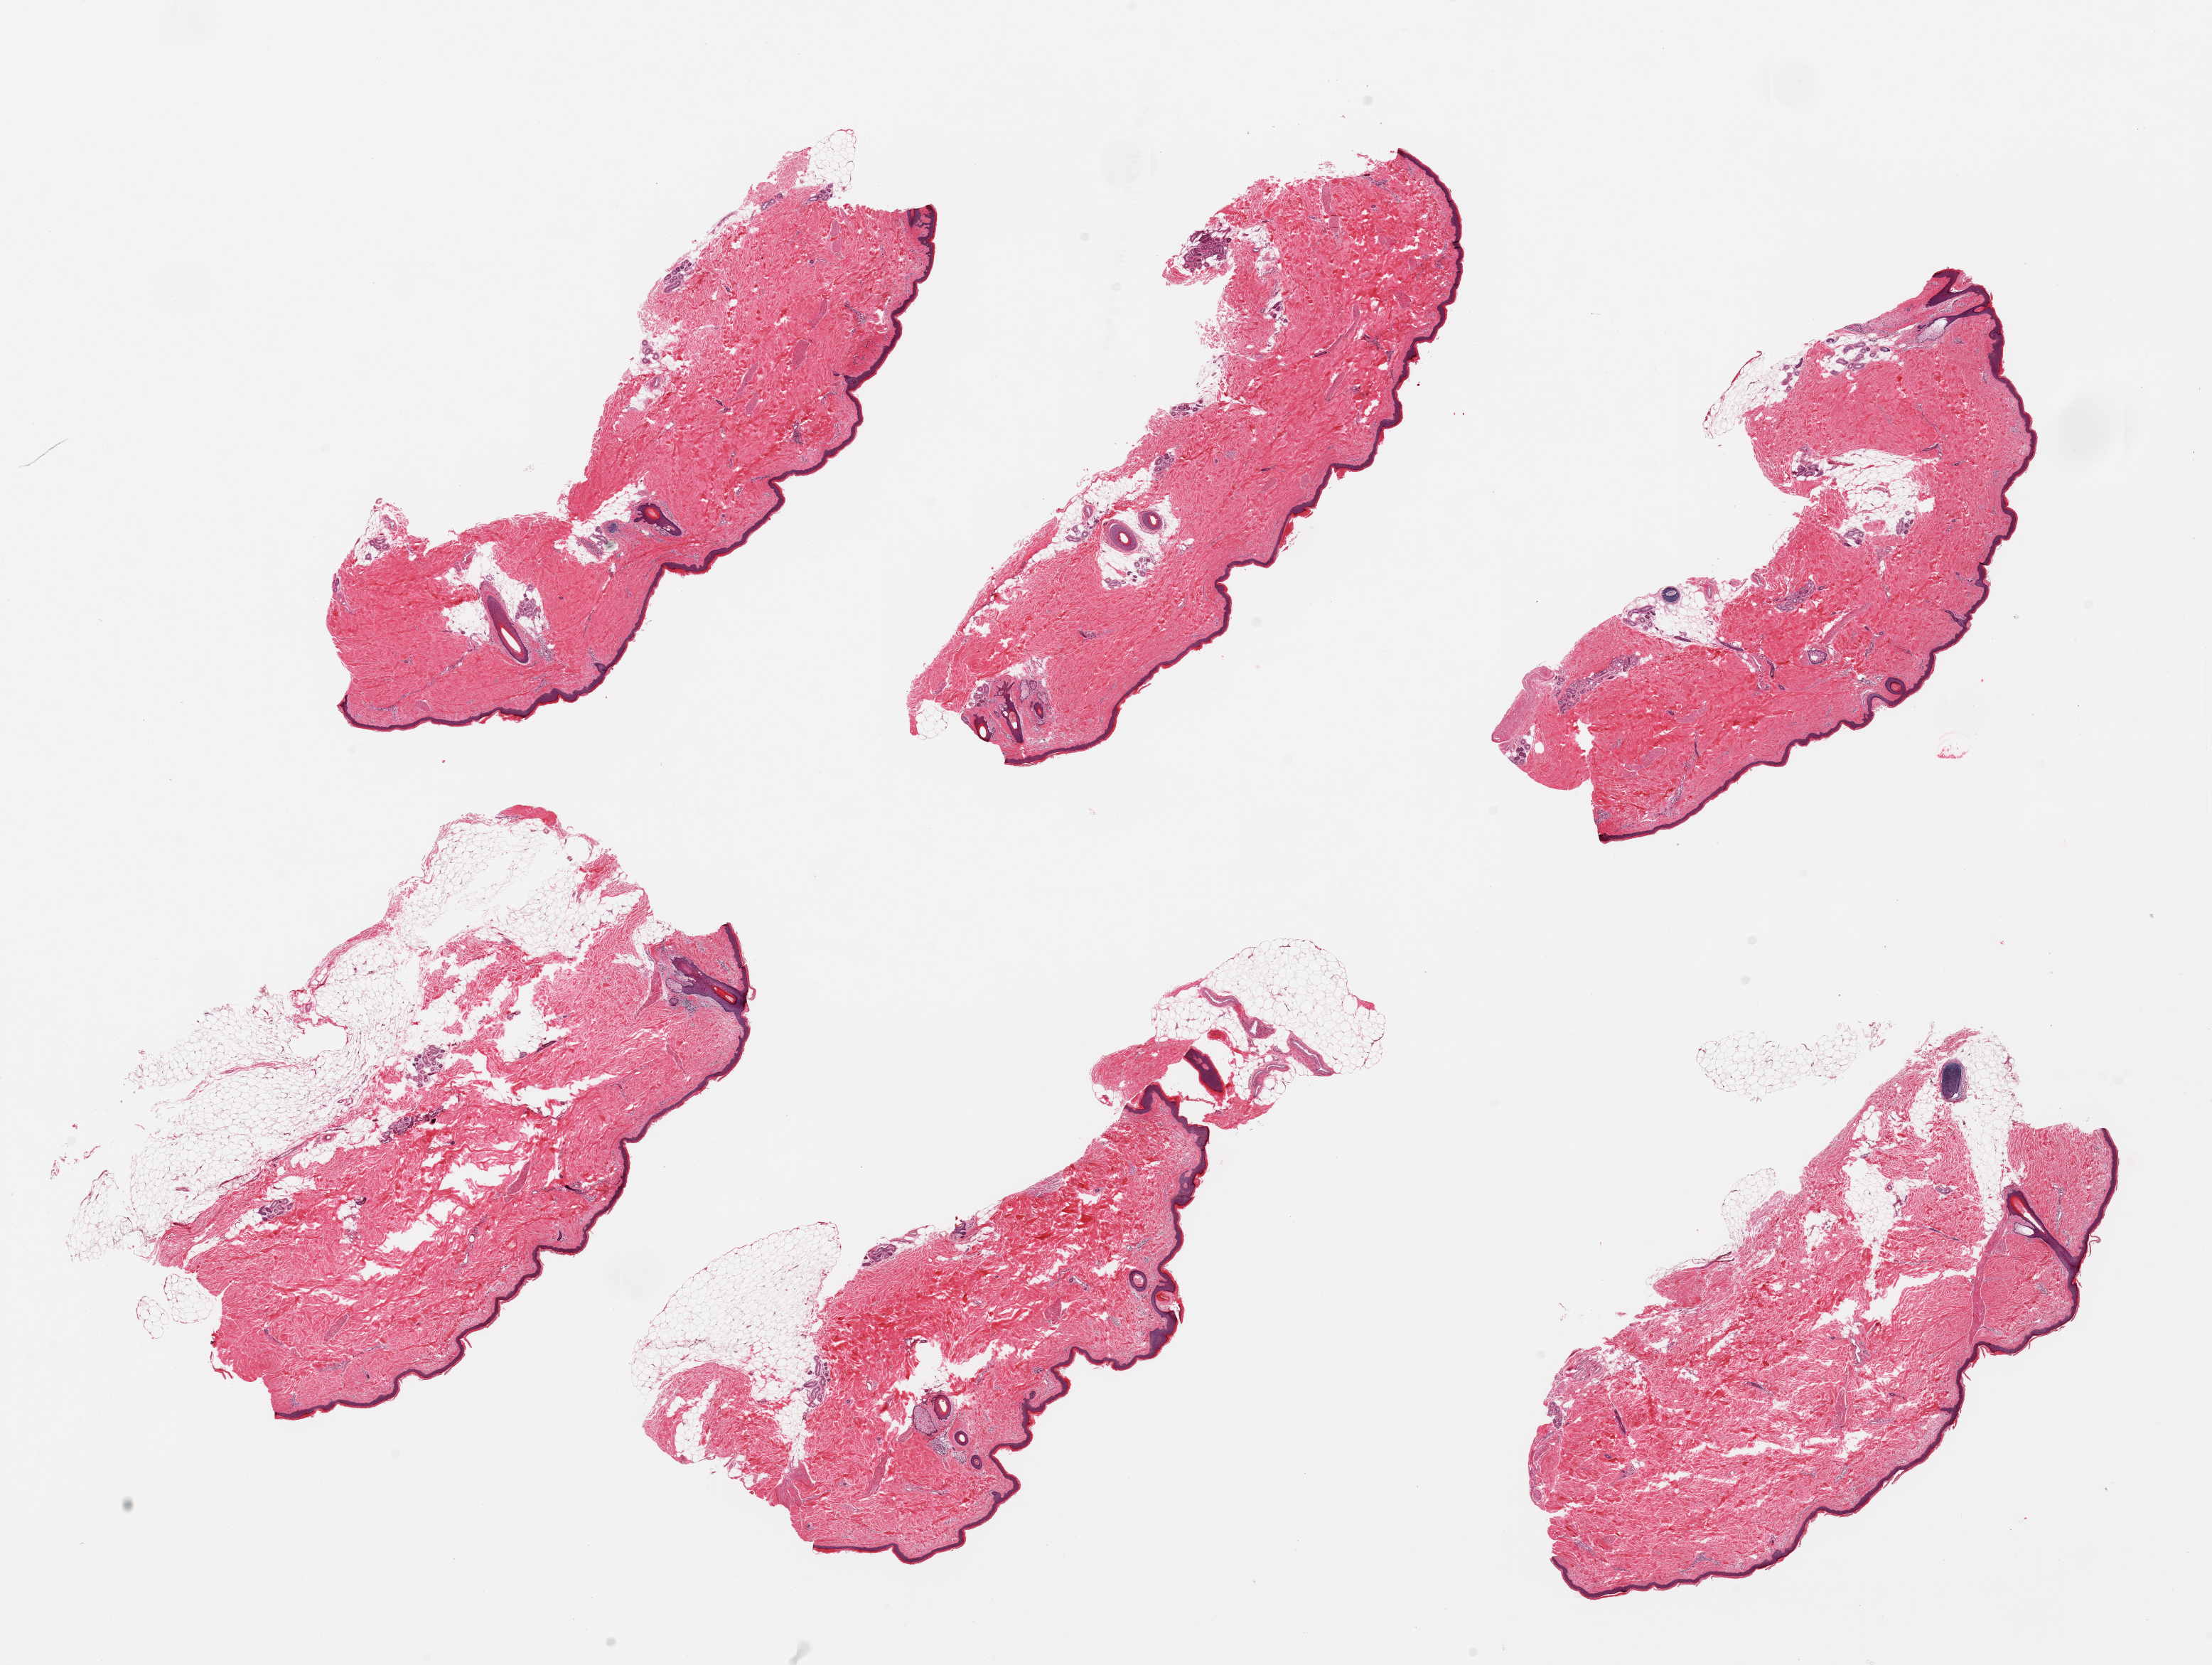
Whole-slide image, hematoxylin and eosin (H&E) stain — low-resolution overview of the scanned area, about 24.6 x 18.5 mm; PAXgene-fixed paraffin-embedded (PFPE) section; target tissue: skin of lower leg; tissue donor sample.
* pathologist's review note for this sample: 6 pieces; up to 25% attached fat on few sections, epidermis measures about 44 microns